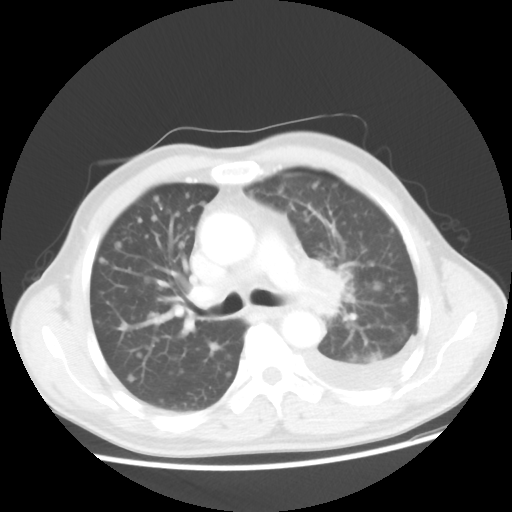
Chest CT, one axial slice; slice 30 of 48 in the series (ordered by position); reconstruction kernel STANDARD; 100 kVp; lung window (W 1500 / L -600 HU); 5 mm slice thickness; 512 × 512 image matrix, field of view 362 × 362 mm. Patient: male, 55 years. From the clinical record (not read from this slice): clinical TNM (as recorded): T2 N3 M1a; histopathological grade: G3.
Annotated regions visible in this slice (rectangle marked by the reading radiologist):
- lung tumour (recorded histology: squamous cell carcinoma): bounding box (x1, y1, x2, y2) in pixels: (310, 250, 362, 321)